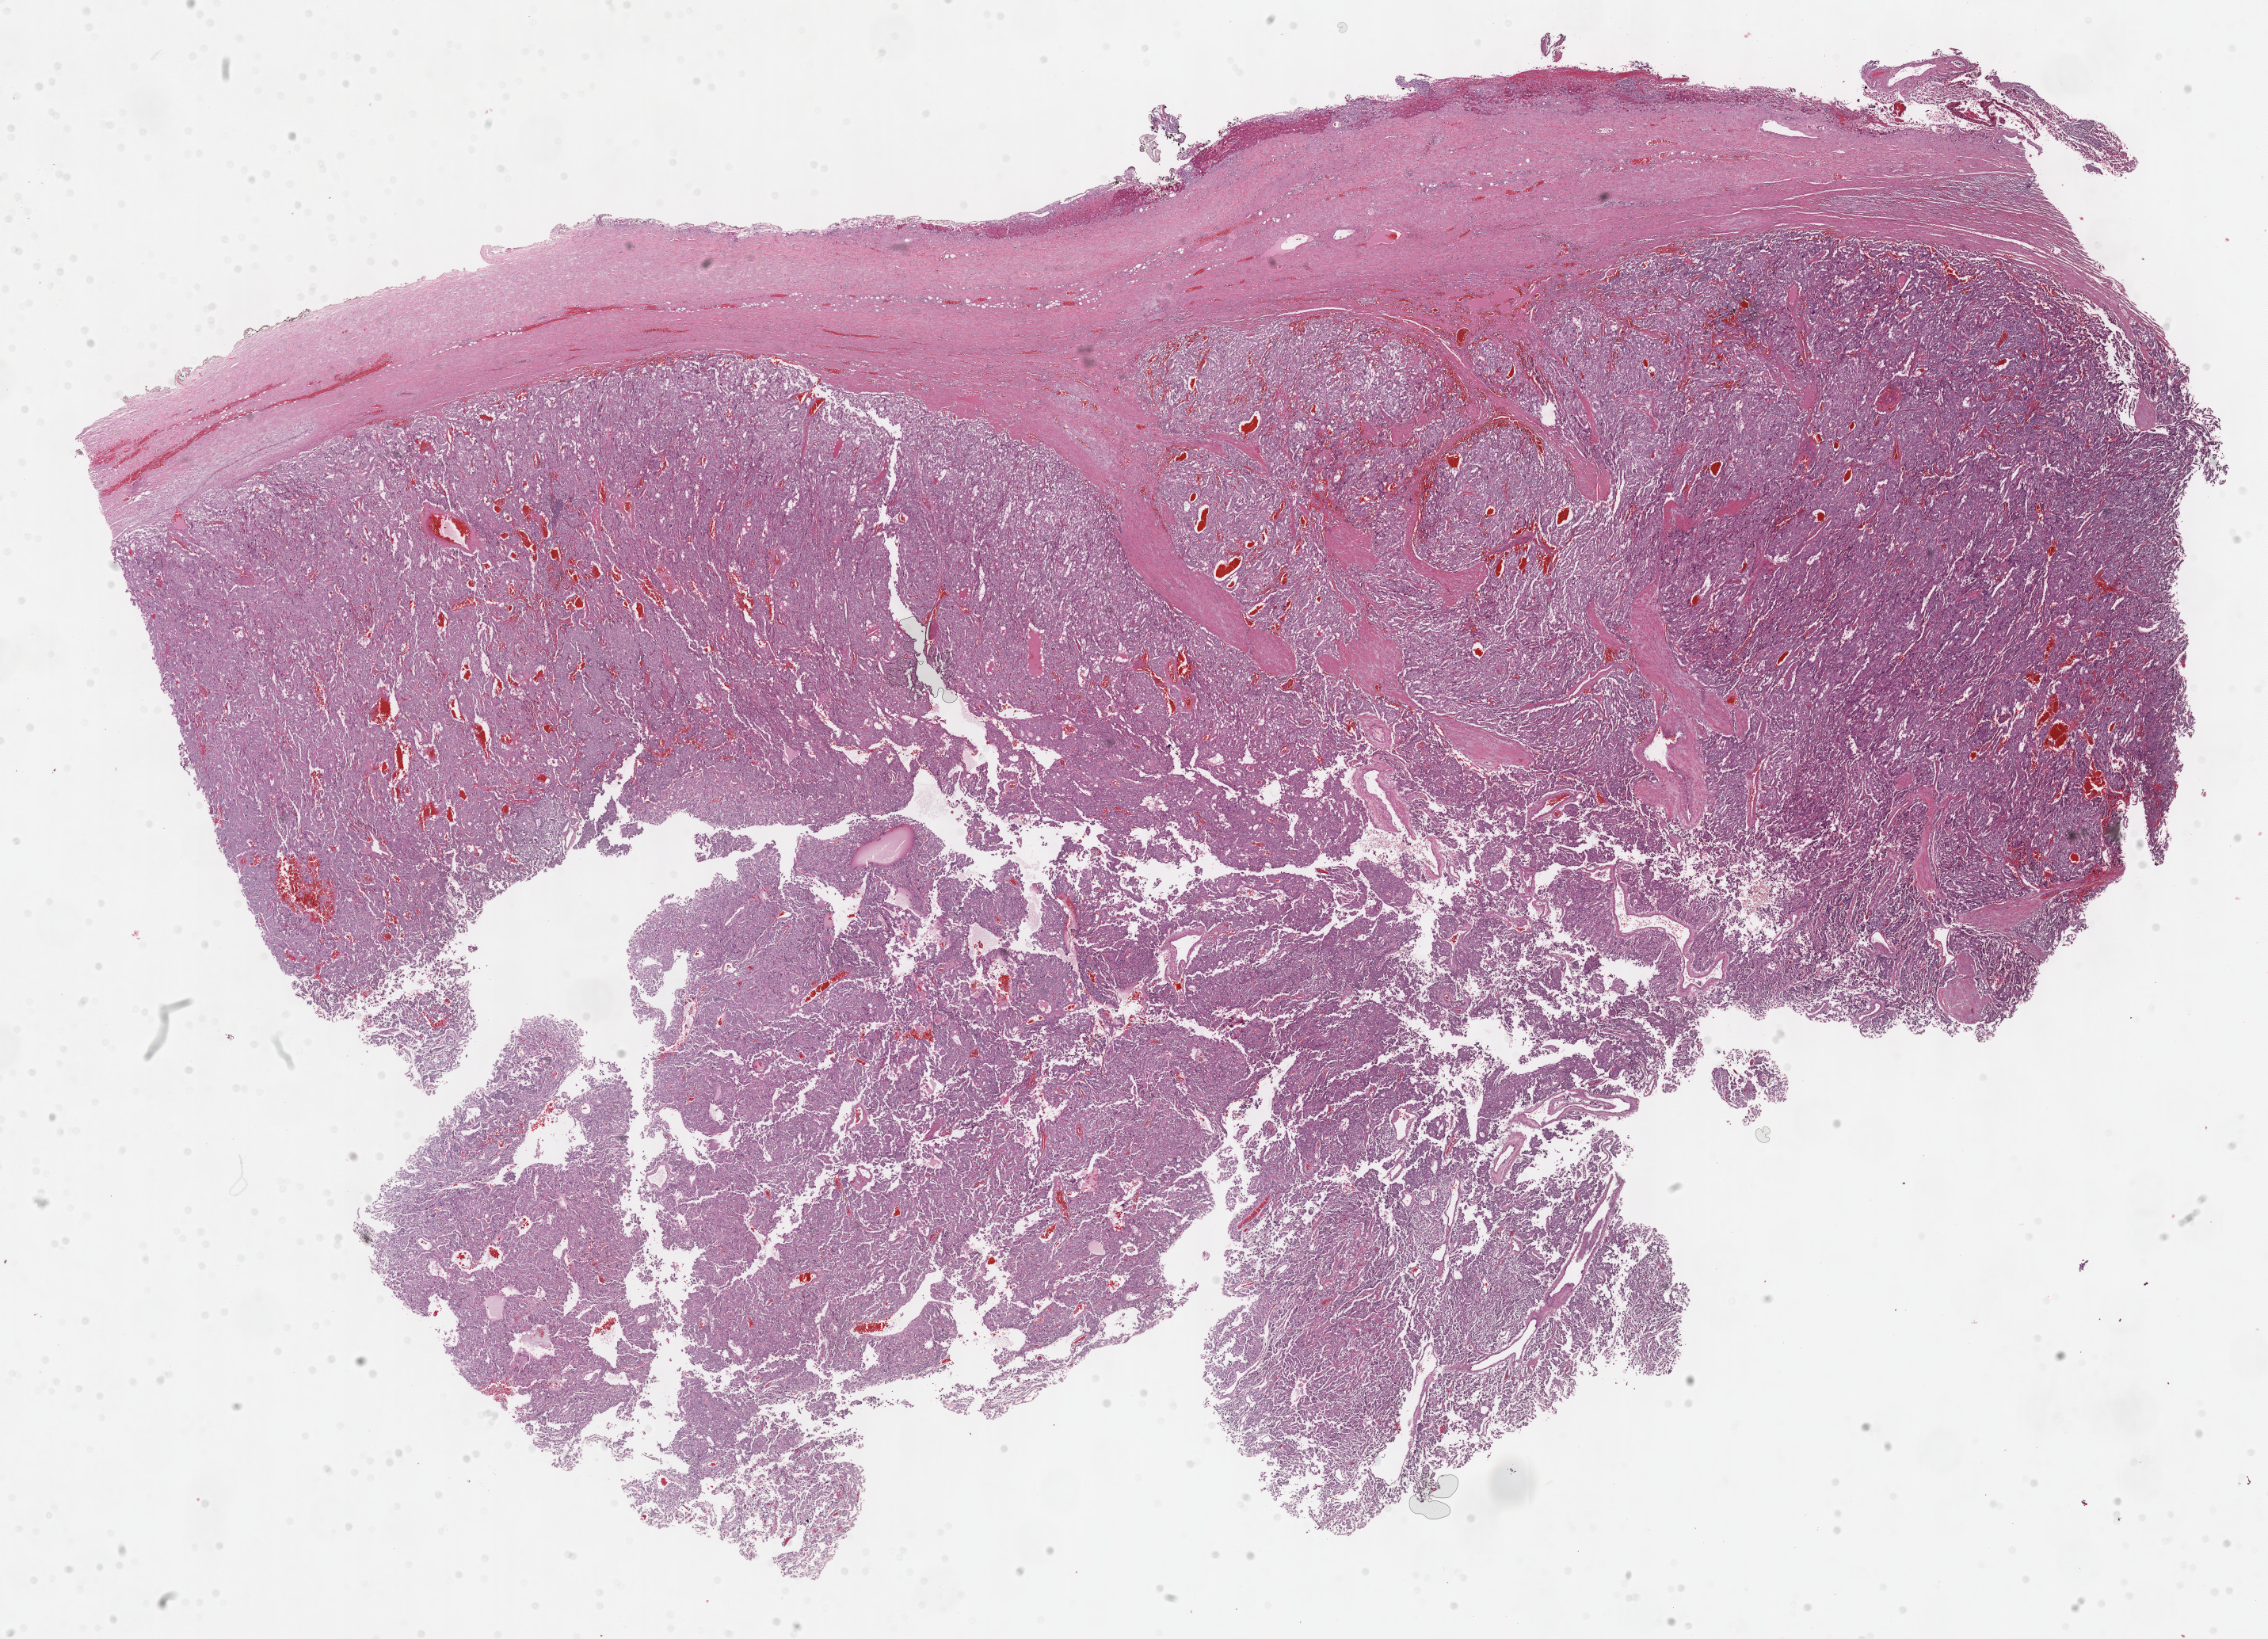
Digitized Hematoxylin and eosin (H&E) stained tissue section (whole slide) — a low-resolution overview of the entire scanned area, about 23.2 x 16.7 mm (acquisition: 40x scan). Formalin-fixed paraffin-embedded (FFPE) diagnostic section. Sample: primary tumour, adrenal gland. Patient: male, age at initial diagnosis 33 years.
Histologic diagnosis: Pheochromocytoma, NOS.